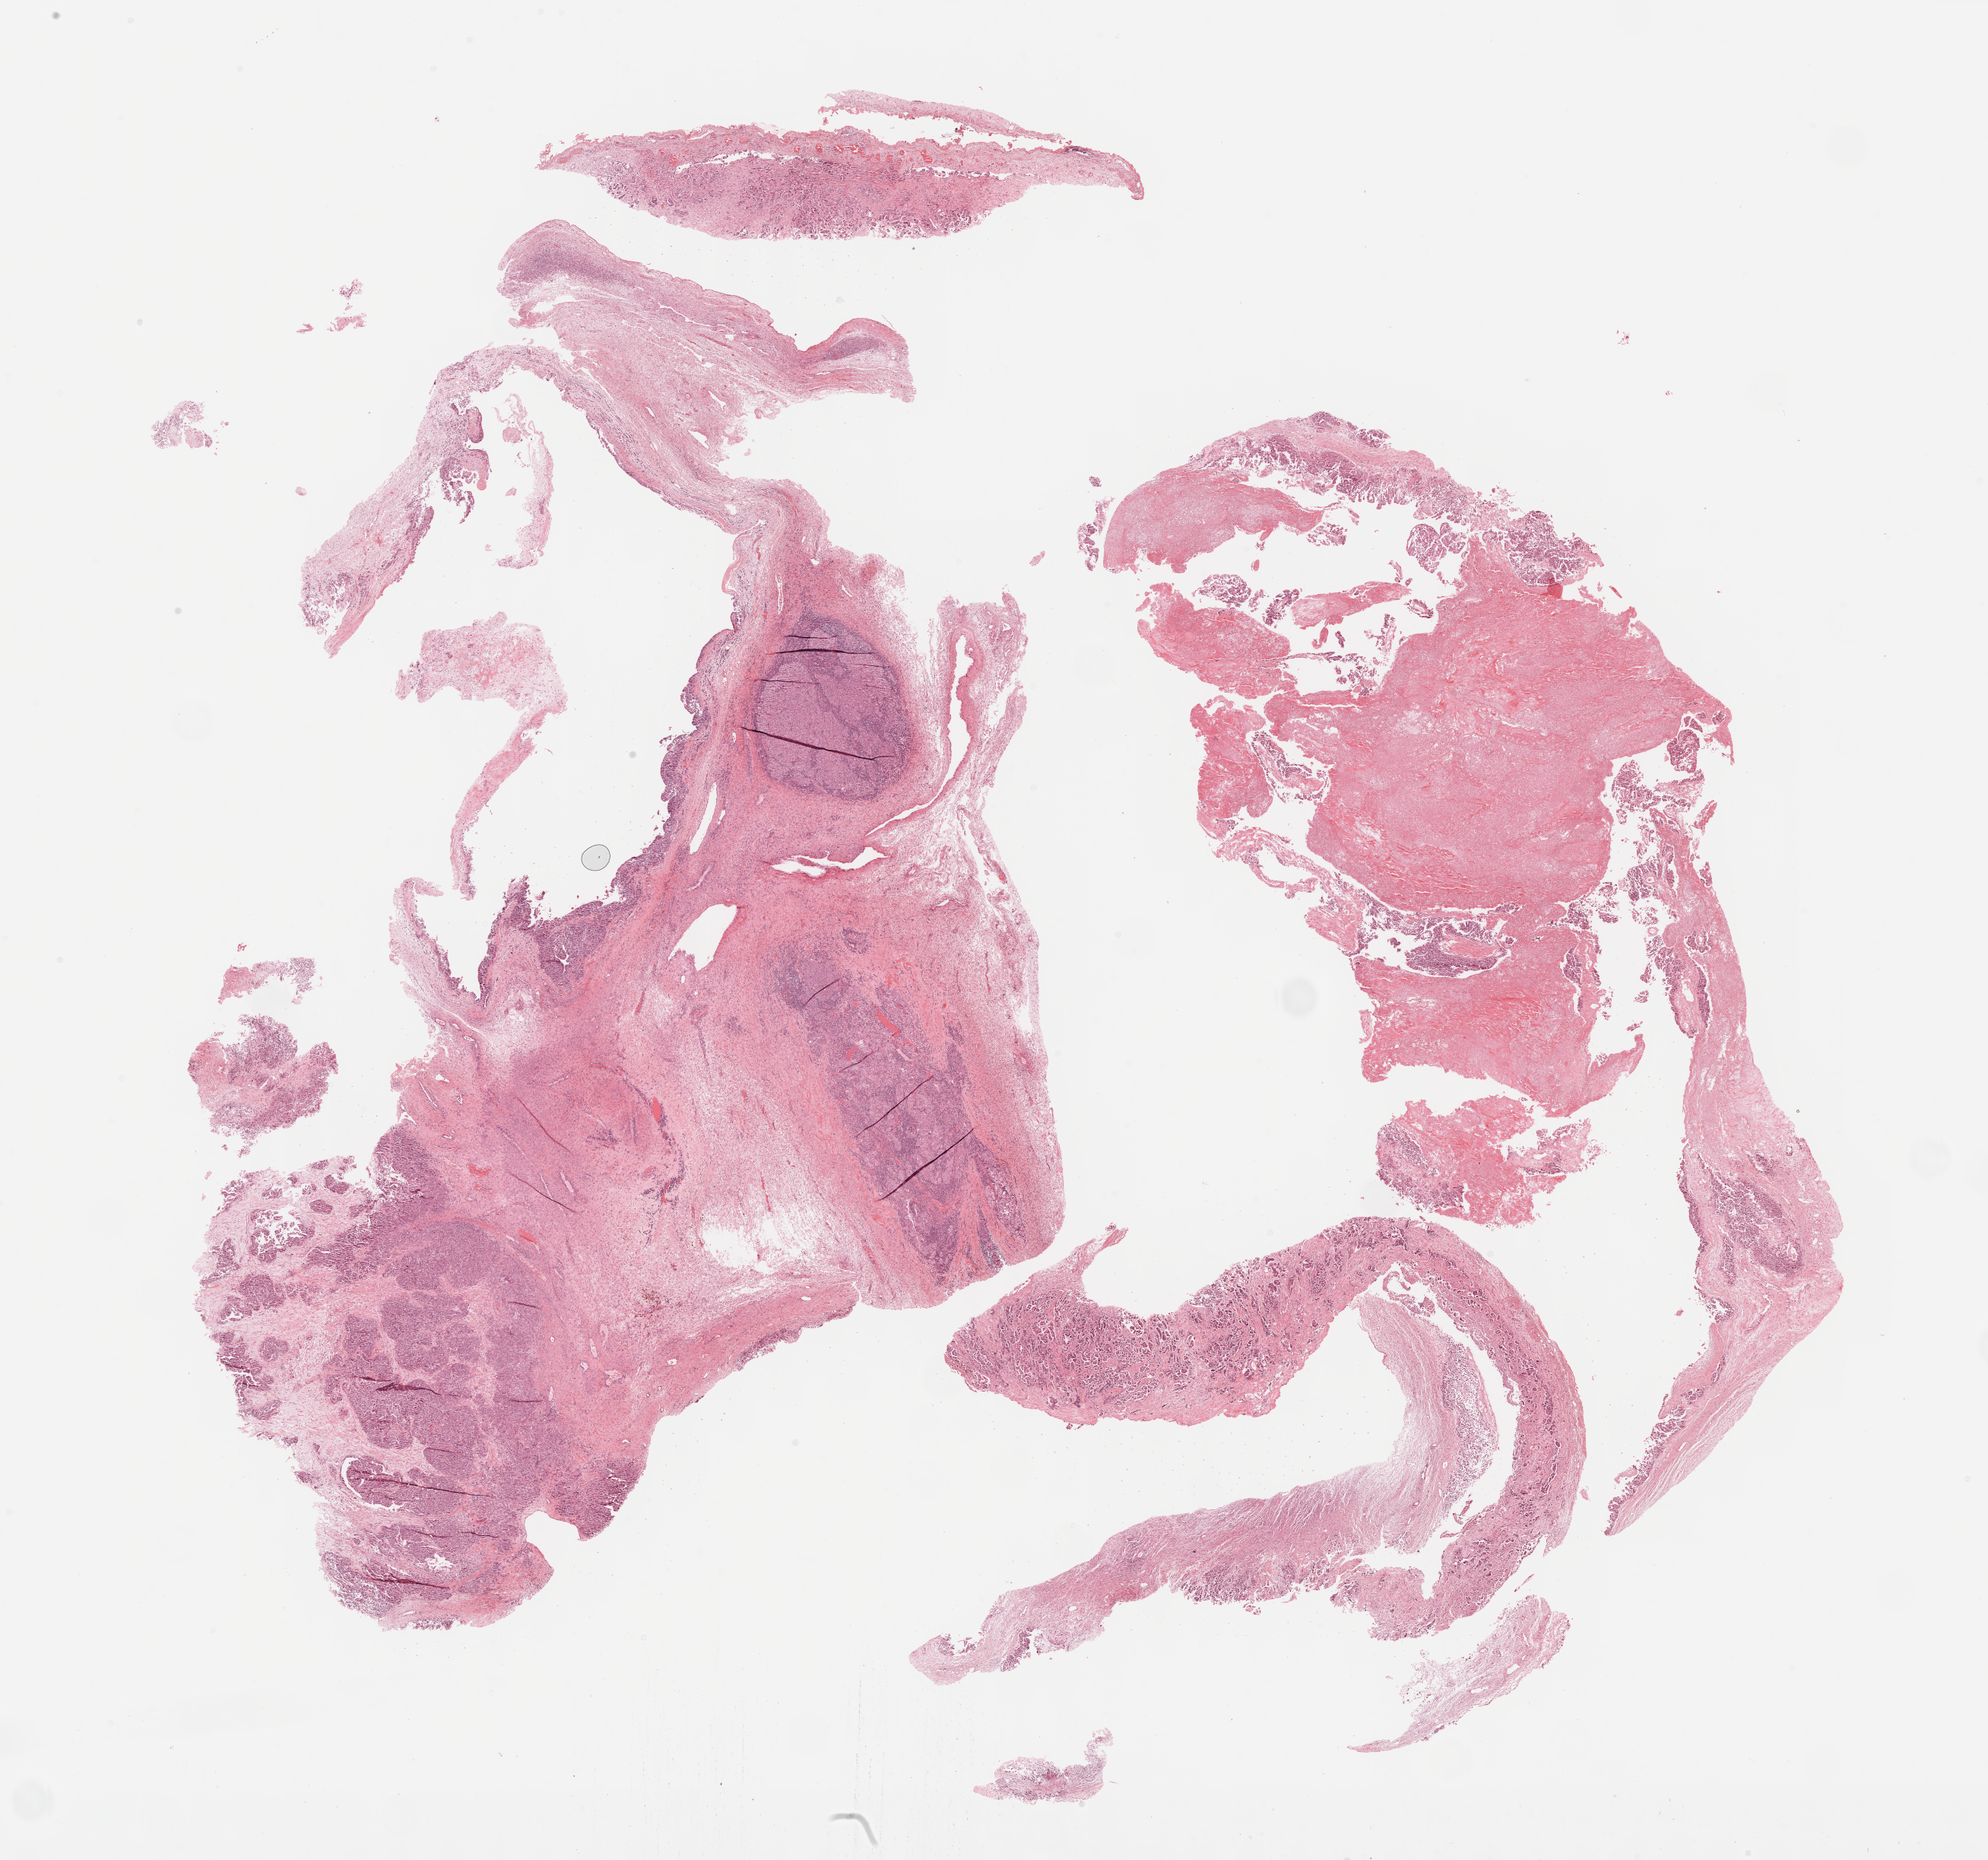
Digitized Hematoxylin and eosin (H&E) stained tissue section (whole slide) — shown as a low-resolution overview of the whole scanned area (about 21.1 x 19.8 mm, from a 40x scan); formalin-fixed paraffin-embedded (FFPE) diagnostic section; primary tumour sample from the ovary. Female, age 61 years at initial diagnosis. Histologic grade: G3 (poorly differentiated).
Pathologic diagnosis: Serous cystadenocarcinoma, NOS. FIGO stage: IIIC.